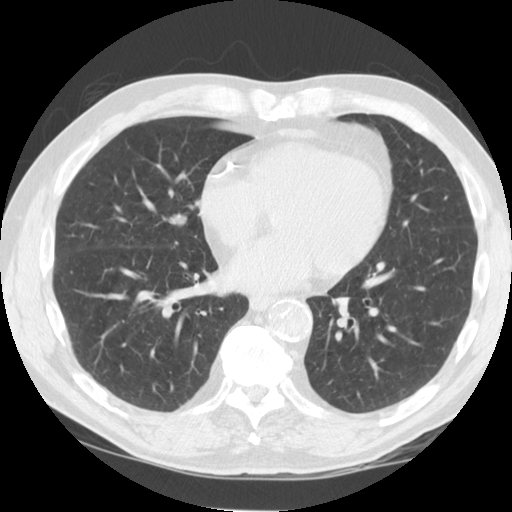
Low-dose screening chest CT, axial slice; third screening round (two years after baseline); lung window (W 1500 / L -600 HU); slice 80 of 125 in the series. Male, age 64 years at enrolment. Current smoker at enrolment.
Lesion marked by an expert reader, bounding box (x1, y1, x2, y2) in pixels: (137, 200, 197, 256). Screening reader's record for this exam (one nodule recorded; not confirmed to be the boxed lesion): non-calcified nodule or mass ≥4 mm, right middle lobe, 21 × 14 mm, smooth margins, soft tissue attenuation, pre-existing on the prior screen: yes; interval growth: yes. Official screen result: positive, other. Later outcome: lung cancer diagnosed 74 days after this screen — non-small cell carcinoma, right middle lobe, poorly differentiated (G3), stage IIIA (AJCC 6th edition), 20 mm at pathology.